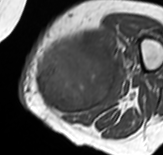
MRI of an extremity soft-tissue mass, one axial slice. Position 25 of 65 along the scan axis. MR volume resampled by the dataset authors to the PET/CT grid (not the native acquisition matrix). 3.27 mm slice thickness. 163 × 155 image matrix, field of view 159 × 151 mm. Female patient. Case-level facts recorded for this patient, not image findings: histological type: pleomorphic leiomyosarcoma; grade: high; site of the primary tumour: left thigh.
Structures marked on this image (expert contour drawn on MRI and transferred to this co-registered scan by the dataset authors):
- gross tumour volume including surrounding oedema: bounding box (x1, y1, x2, y2) in pixels: (33, 31, 120, 114)
- gross tumour volume (mass): (33, 35, 118, 114)